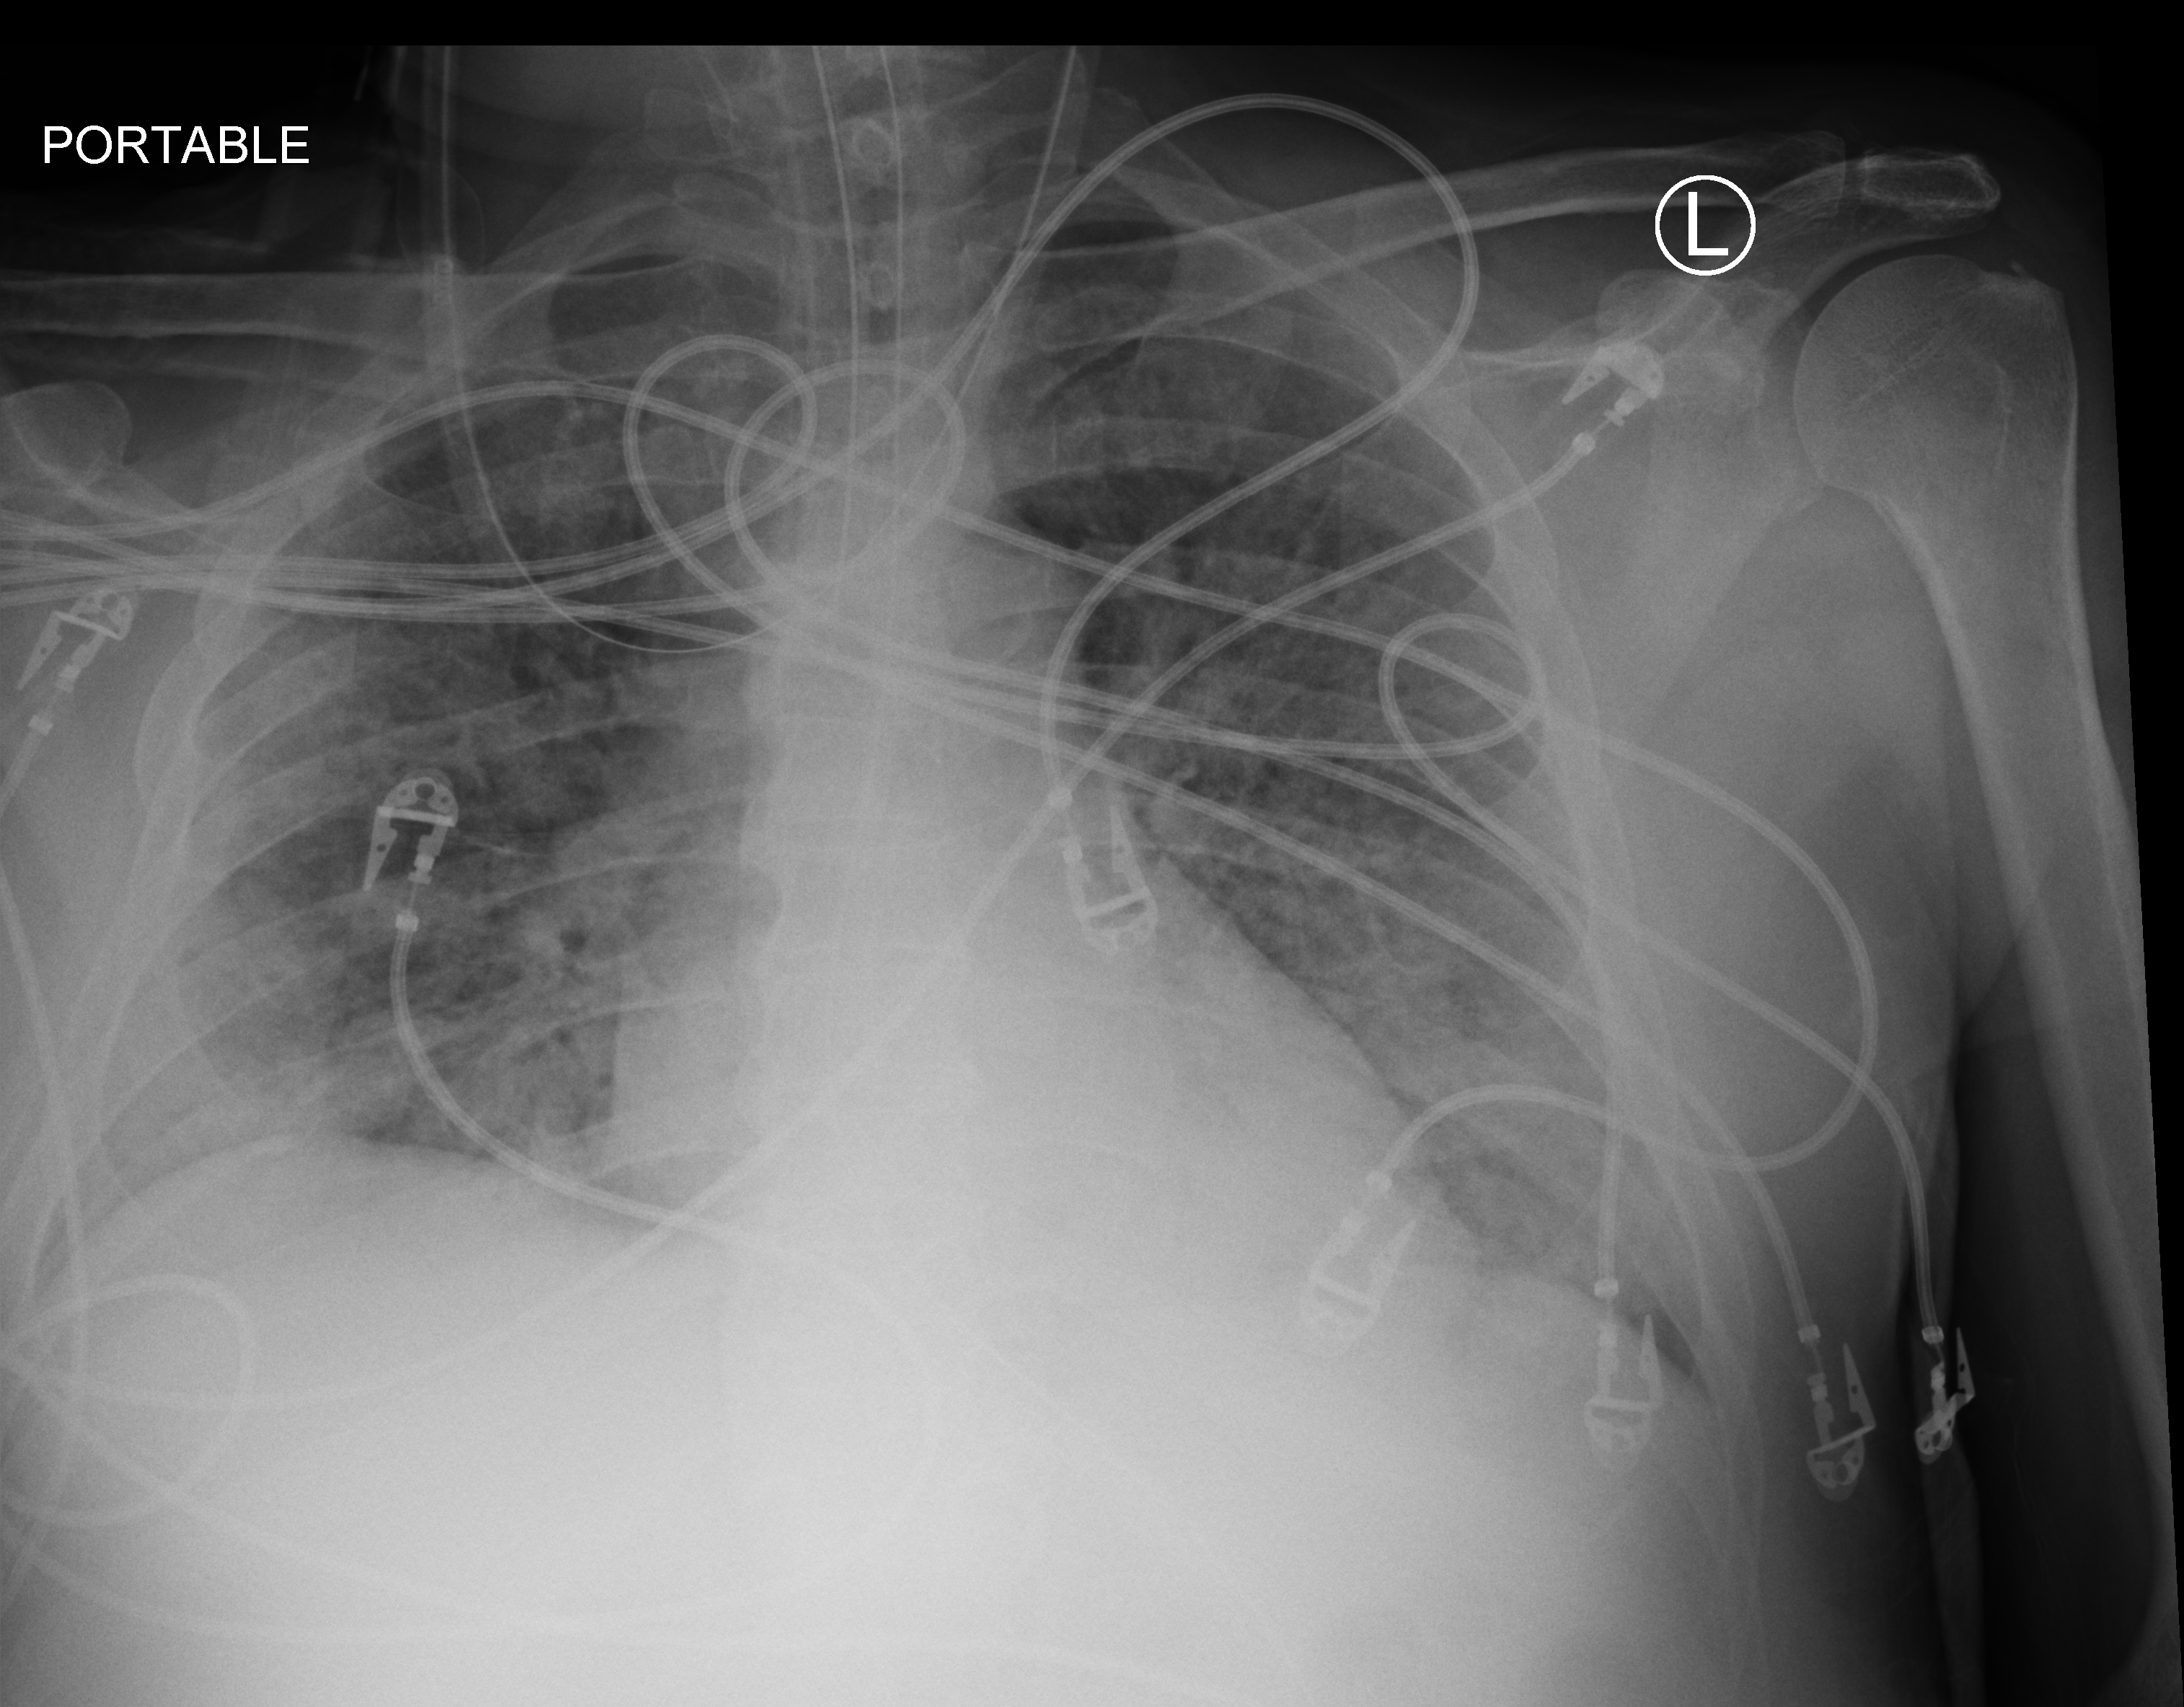
Chest X-ray (portable); anteroposterior (AP) projection. Male patient hospitalised with COVID-19, age 60–74 years.
From the hospital-stay record, not from the radiograph (when in the stay this image was taken is not recorded):
- mechanically ventilated during this hospital stay: yes
- length of hospital stay: 15 days